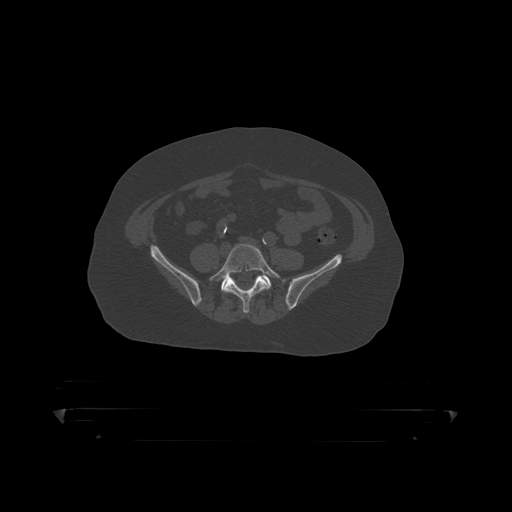
CT including the spine, one axial slice. Position 39 of 390 along the scan axis. 120 kVp. Bone window (W 1800 / L 400 HU). 512 × 512 image matrix. Patient: male, 60 years. Case-level facts recorded for this patient, not image findings: primary cancer: prostate.
Outlined on this slice (semi-automatically segmented with operator editing):
- L5 vertebra: bounding box [x1, y1, x2, y2] px = [209, 243, 281, 314]